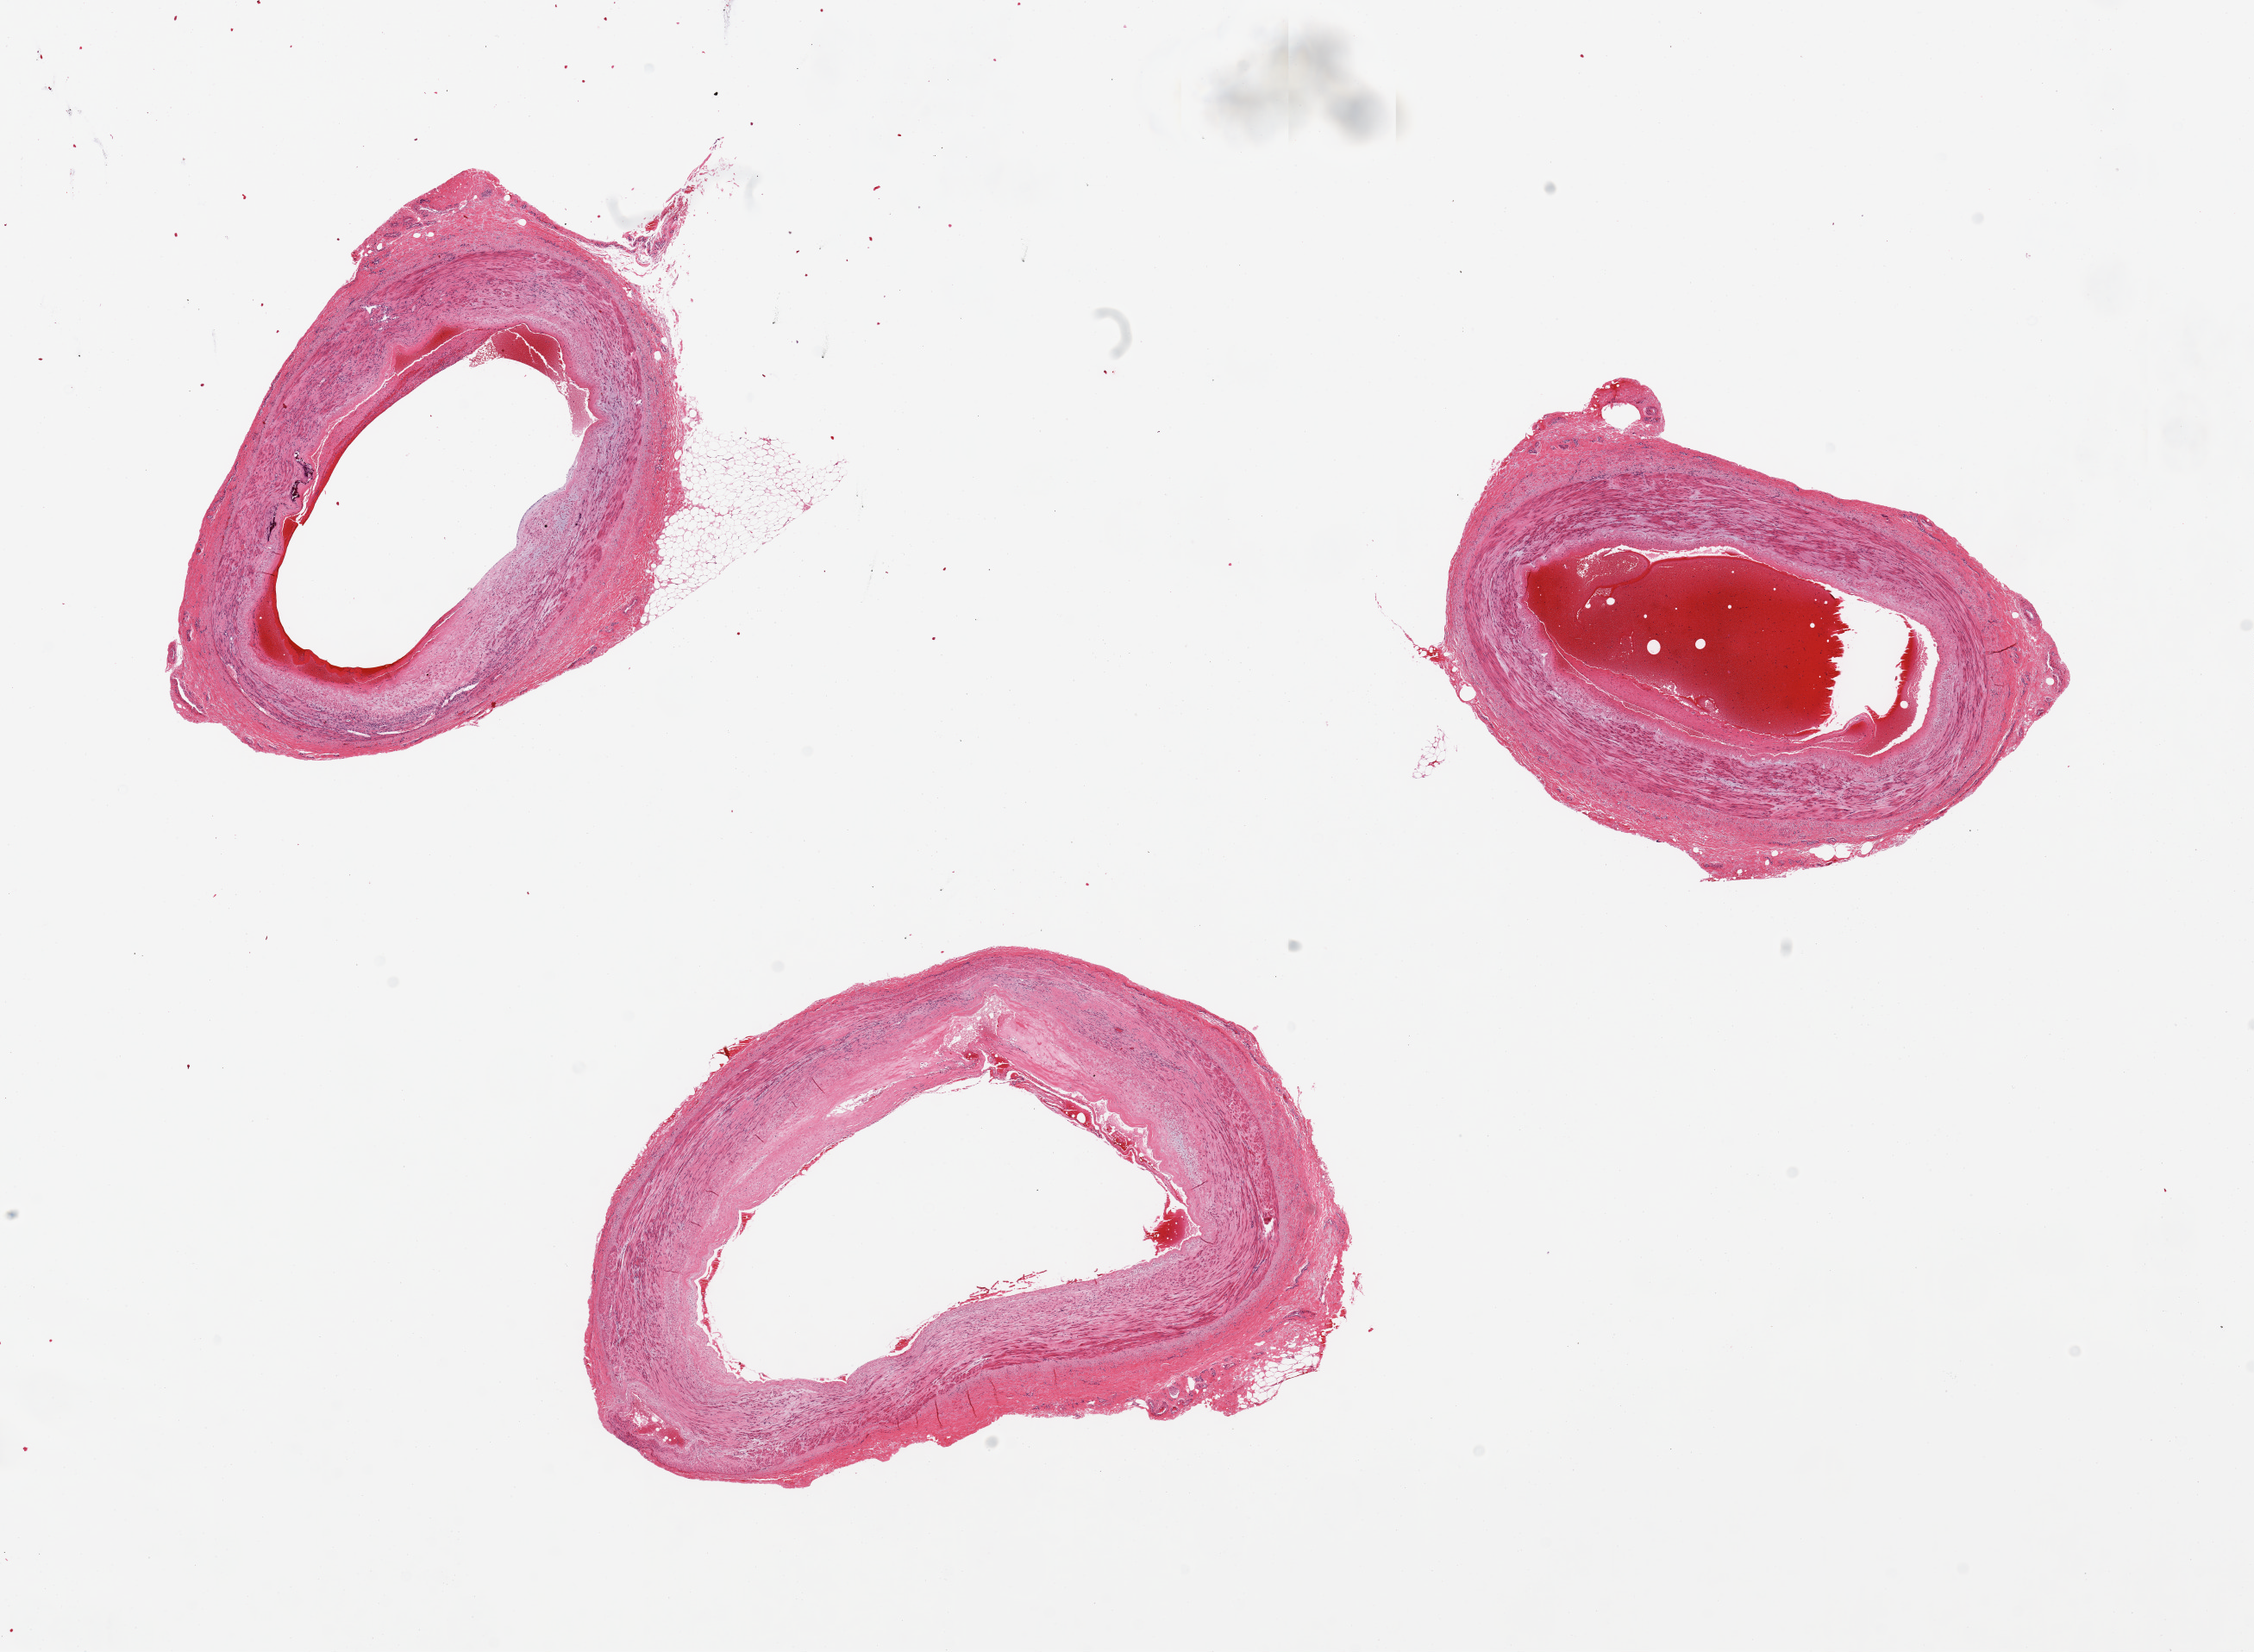
Haematoxylin and eosin whole-slide image — low-resolution overview of the scanned area, about 20.7 x 15.2 mm, PAXgene-fixed, paraffin-embedded tissue, target tissue: tibial artery, donor tissue sample. Donor: female.
Review note (as recorded): 3 pieces, generally clean specimens.